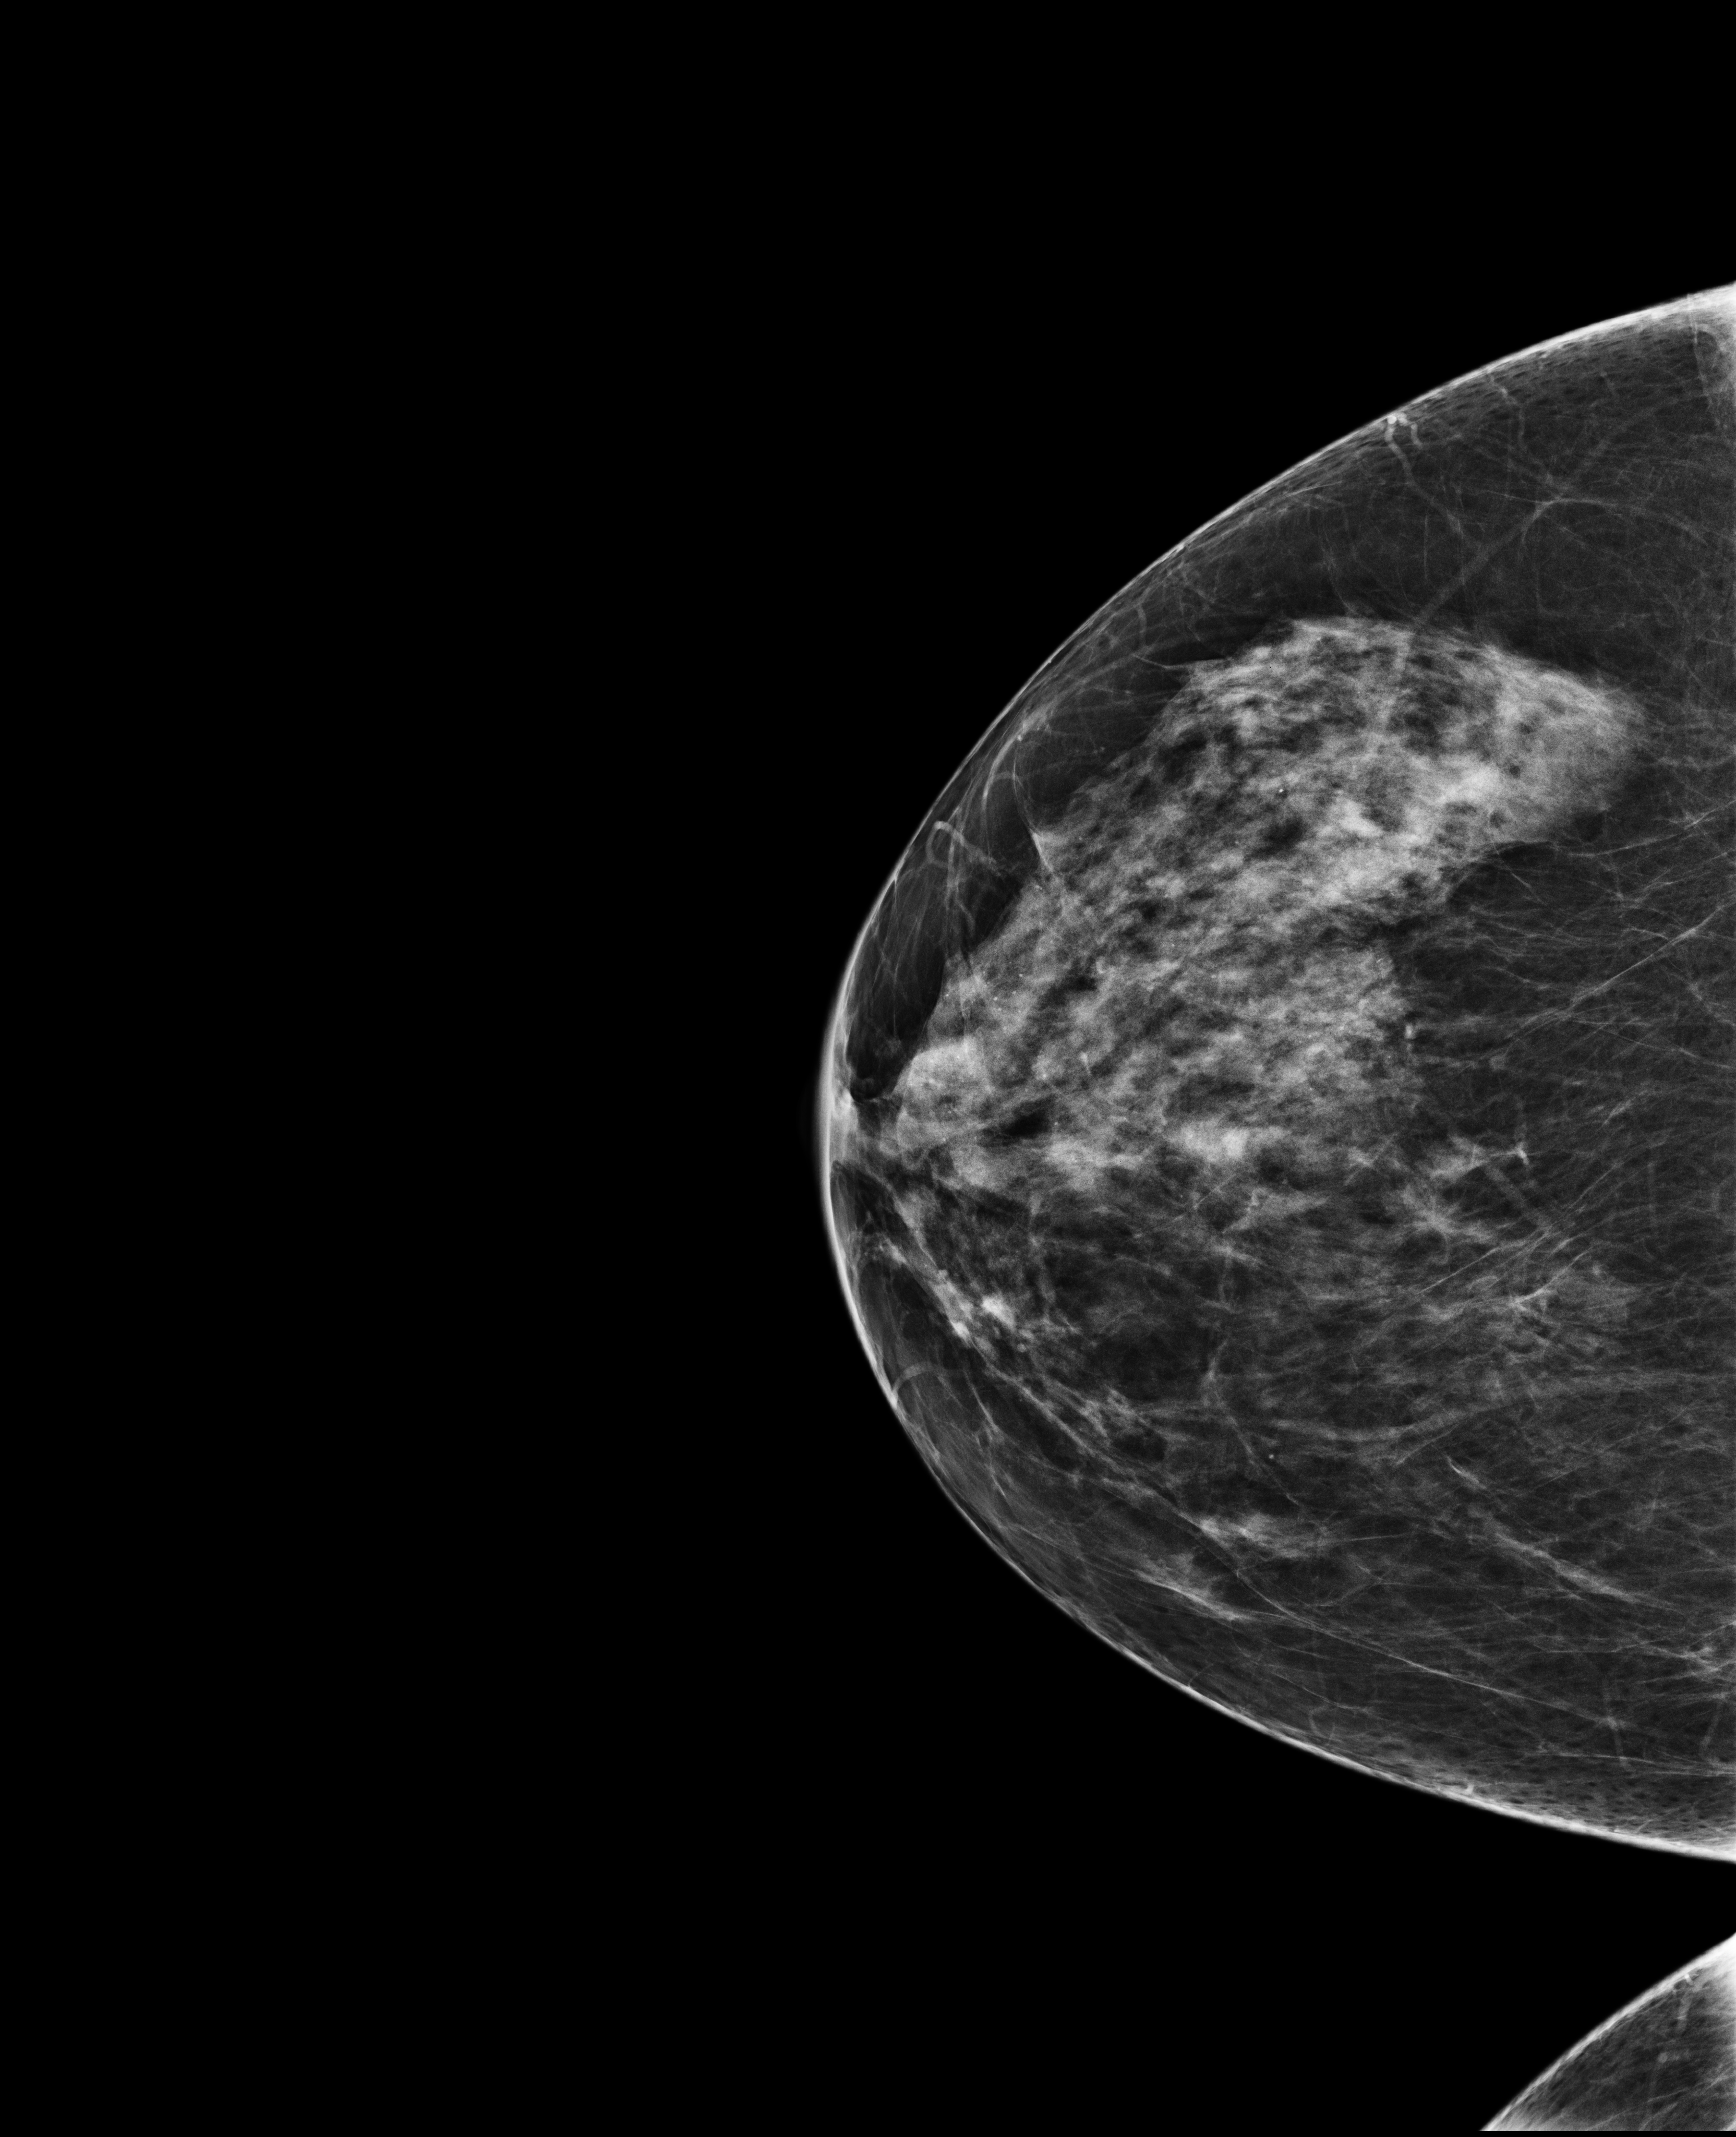
Annual screening mammography examination, compressed breast thickness 66 mm.
Image type: full-field digital mammogram. Breast: right. Projection: cranio-caudal projection.